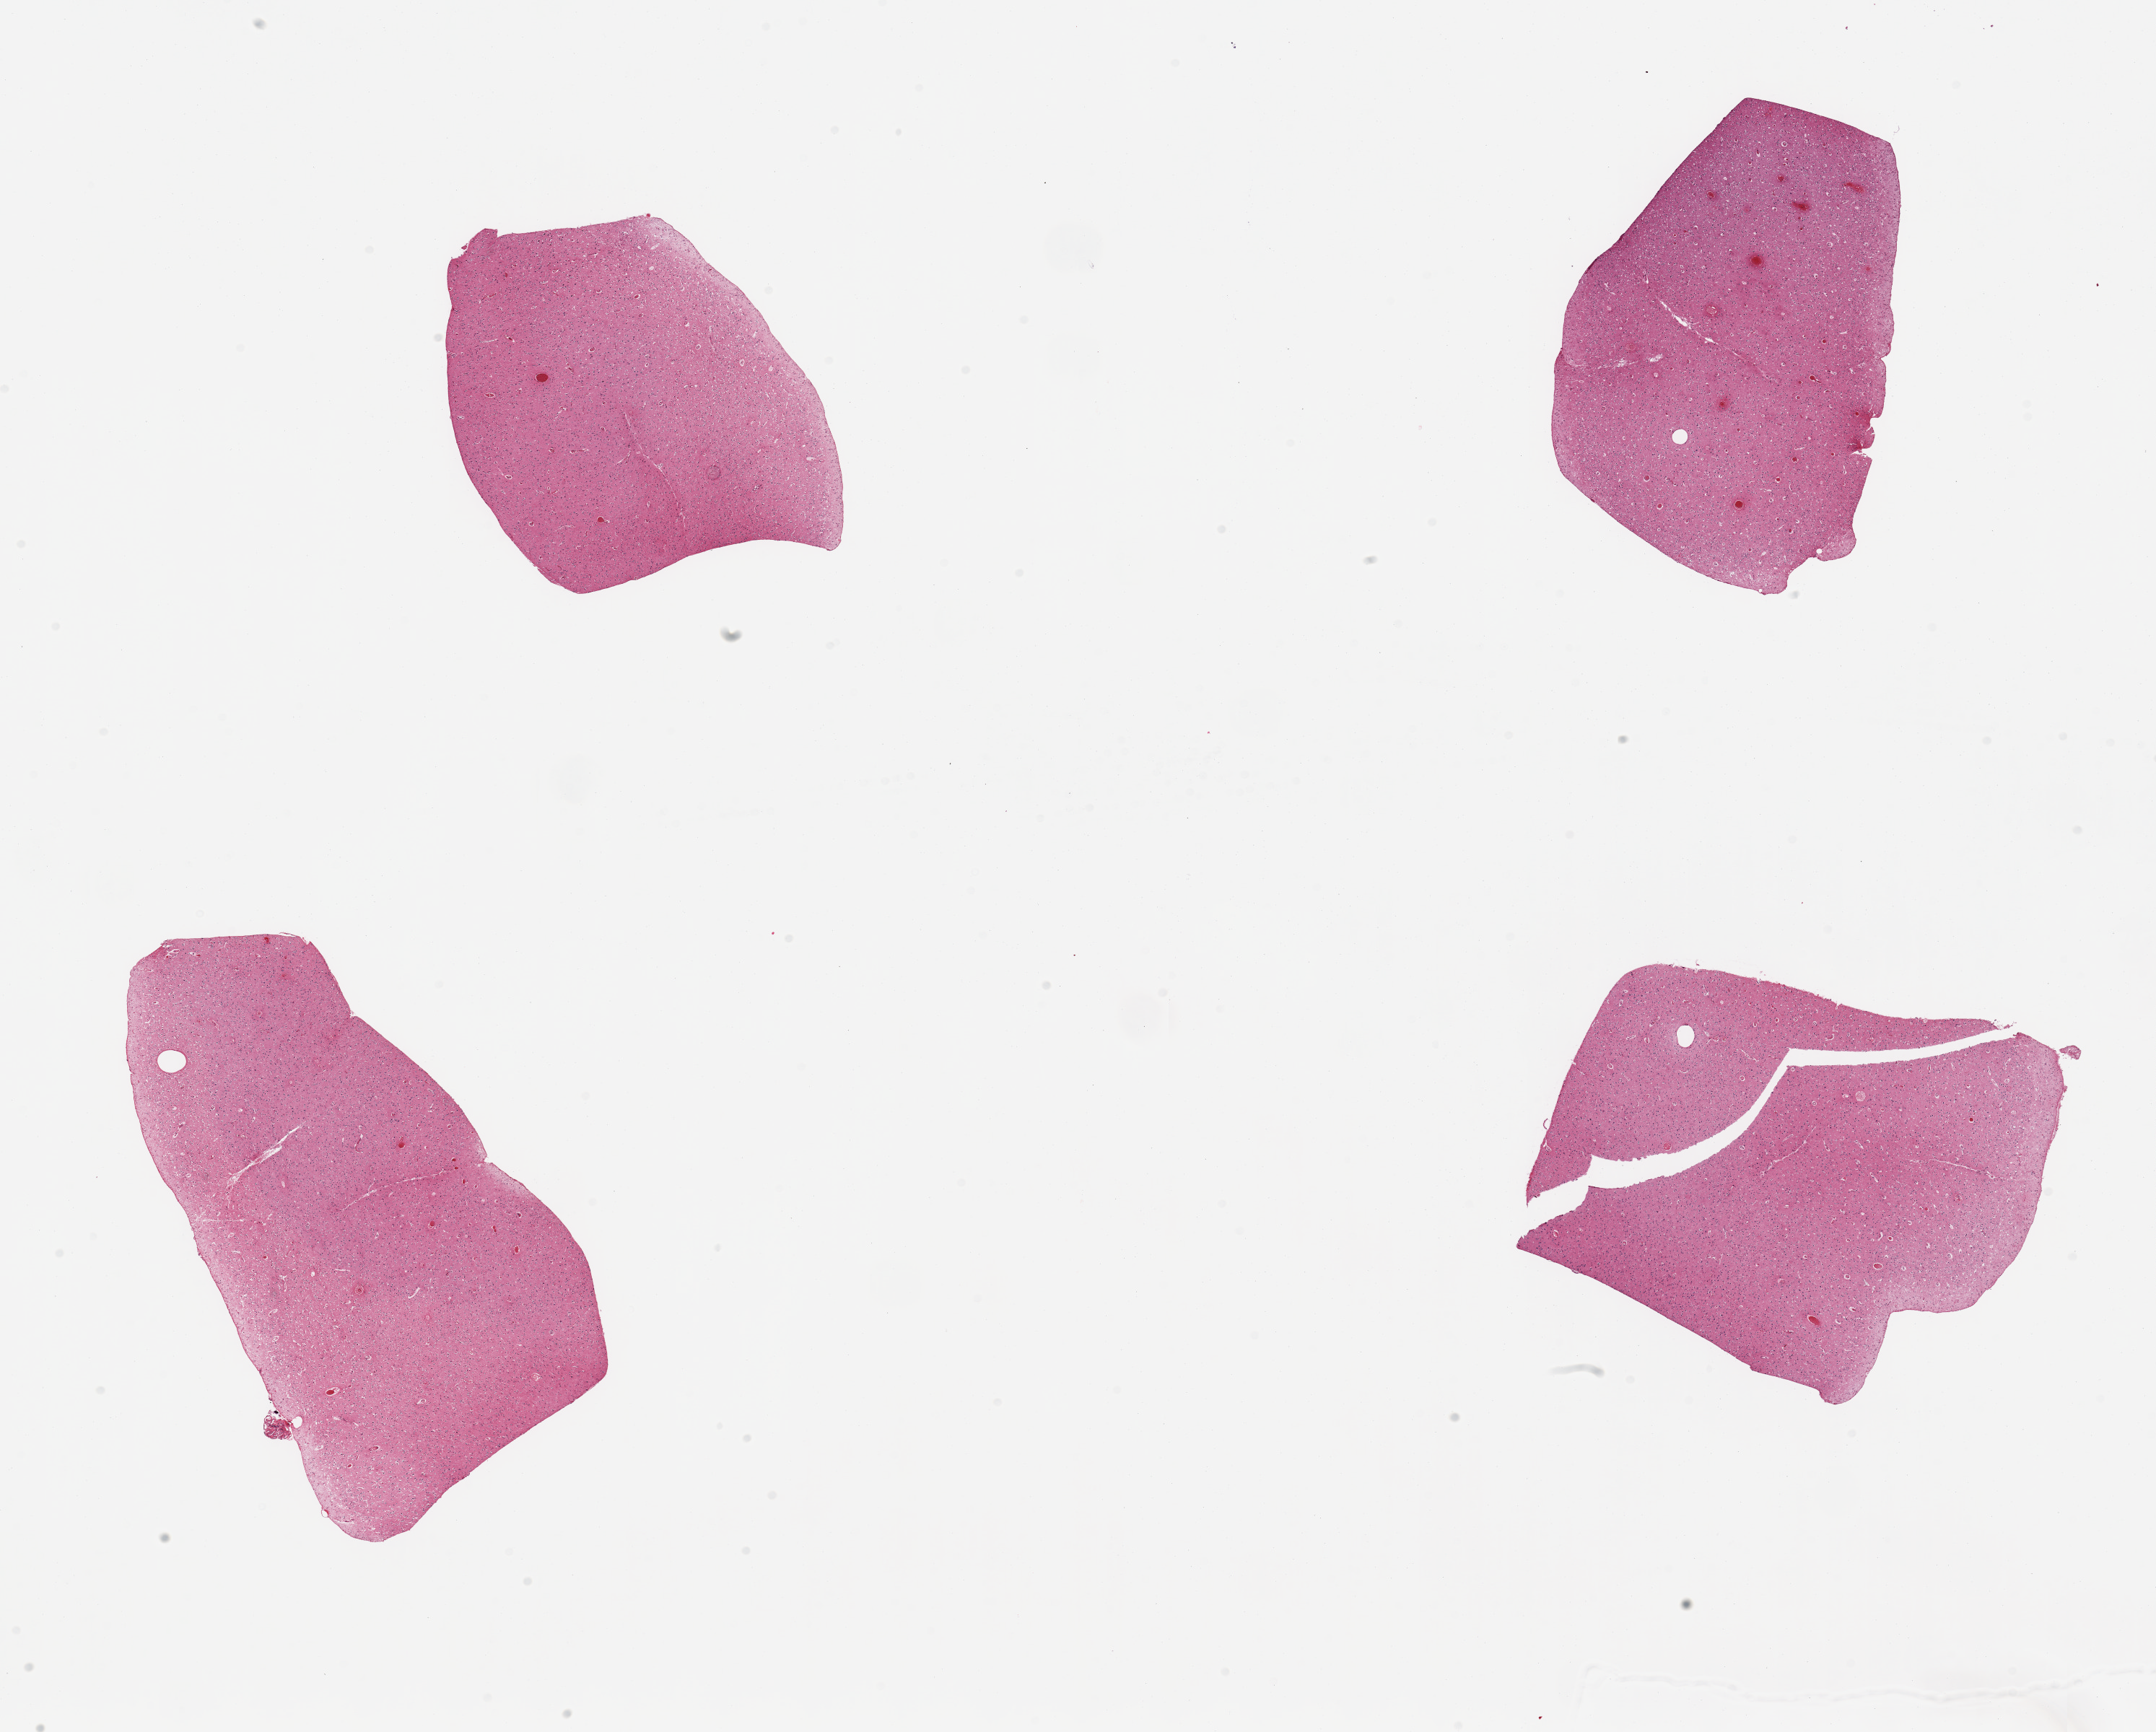
Whole-slide image, H&E stain — a low-resolution overview of the entire scanned area, about 23.6 x 19.0 mm (acquisition: 20x scan). PAXgene-fixed, paraffin-embedded tissue. Target tissue: cerebral cortex. Donor tissue sample. Donor sex: male.
Review note (as recorded): 4 pieces.